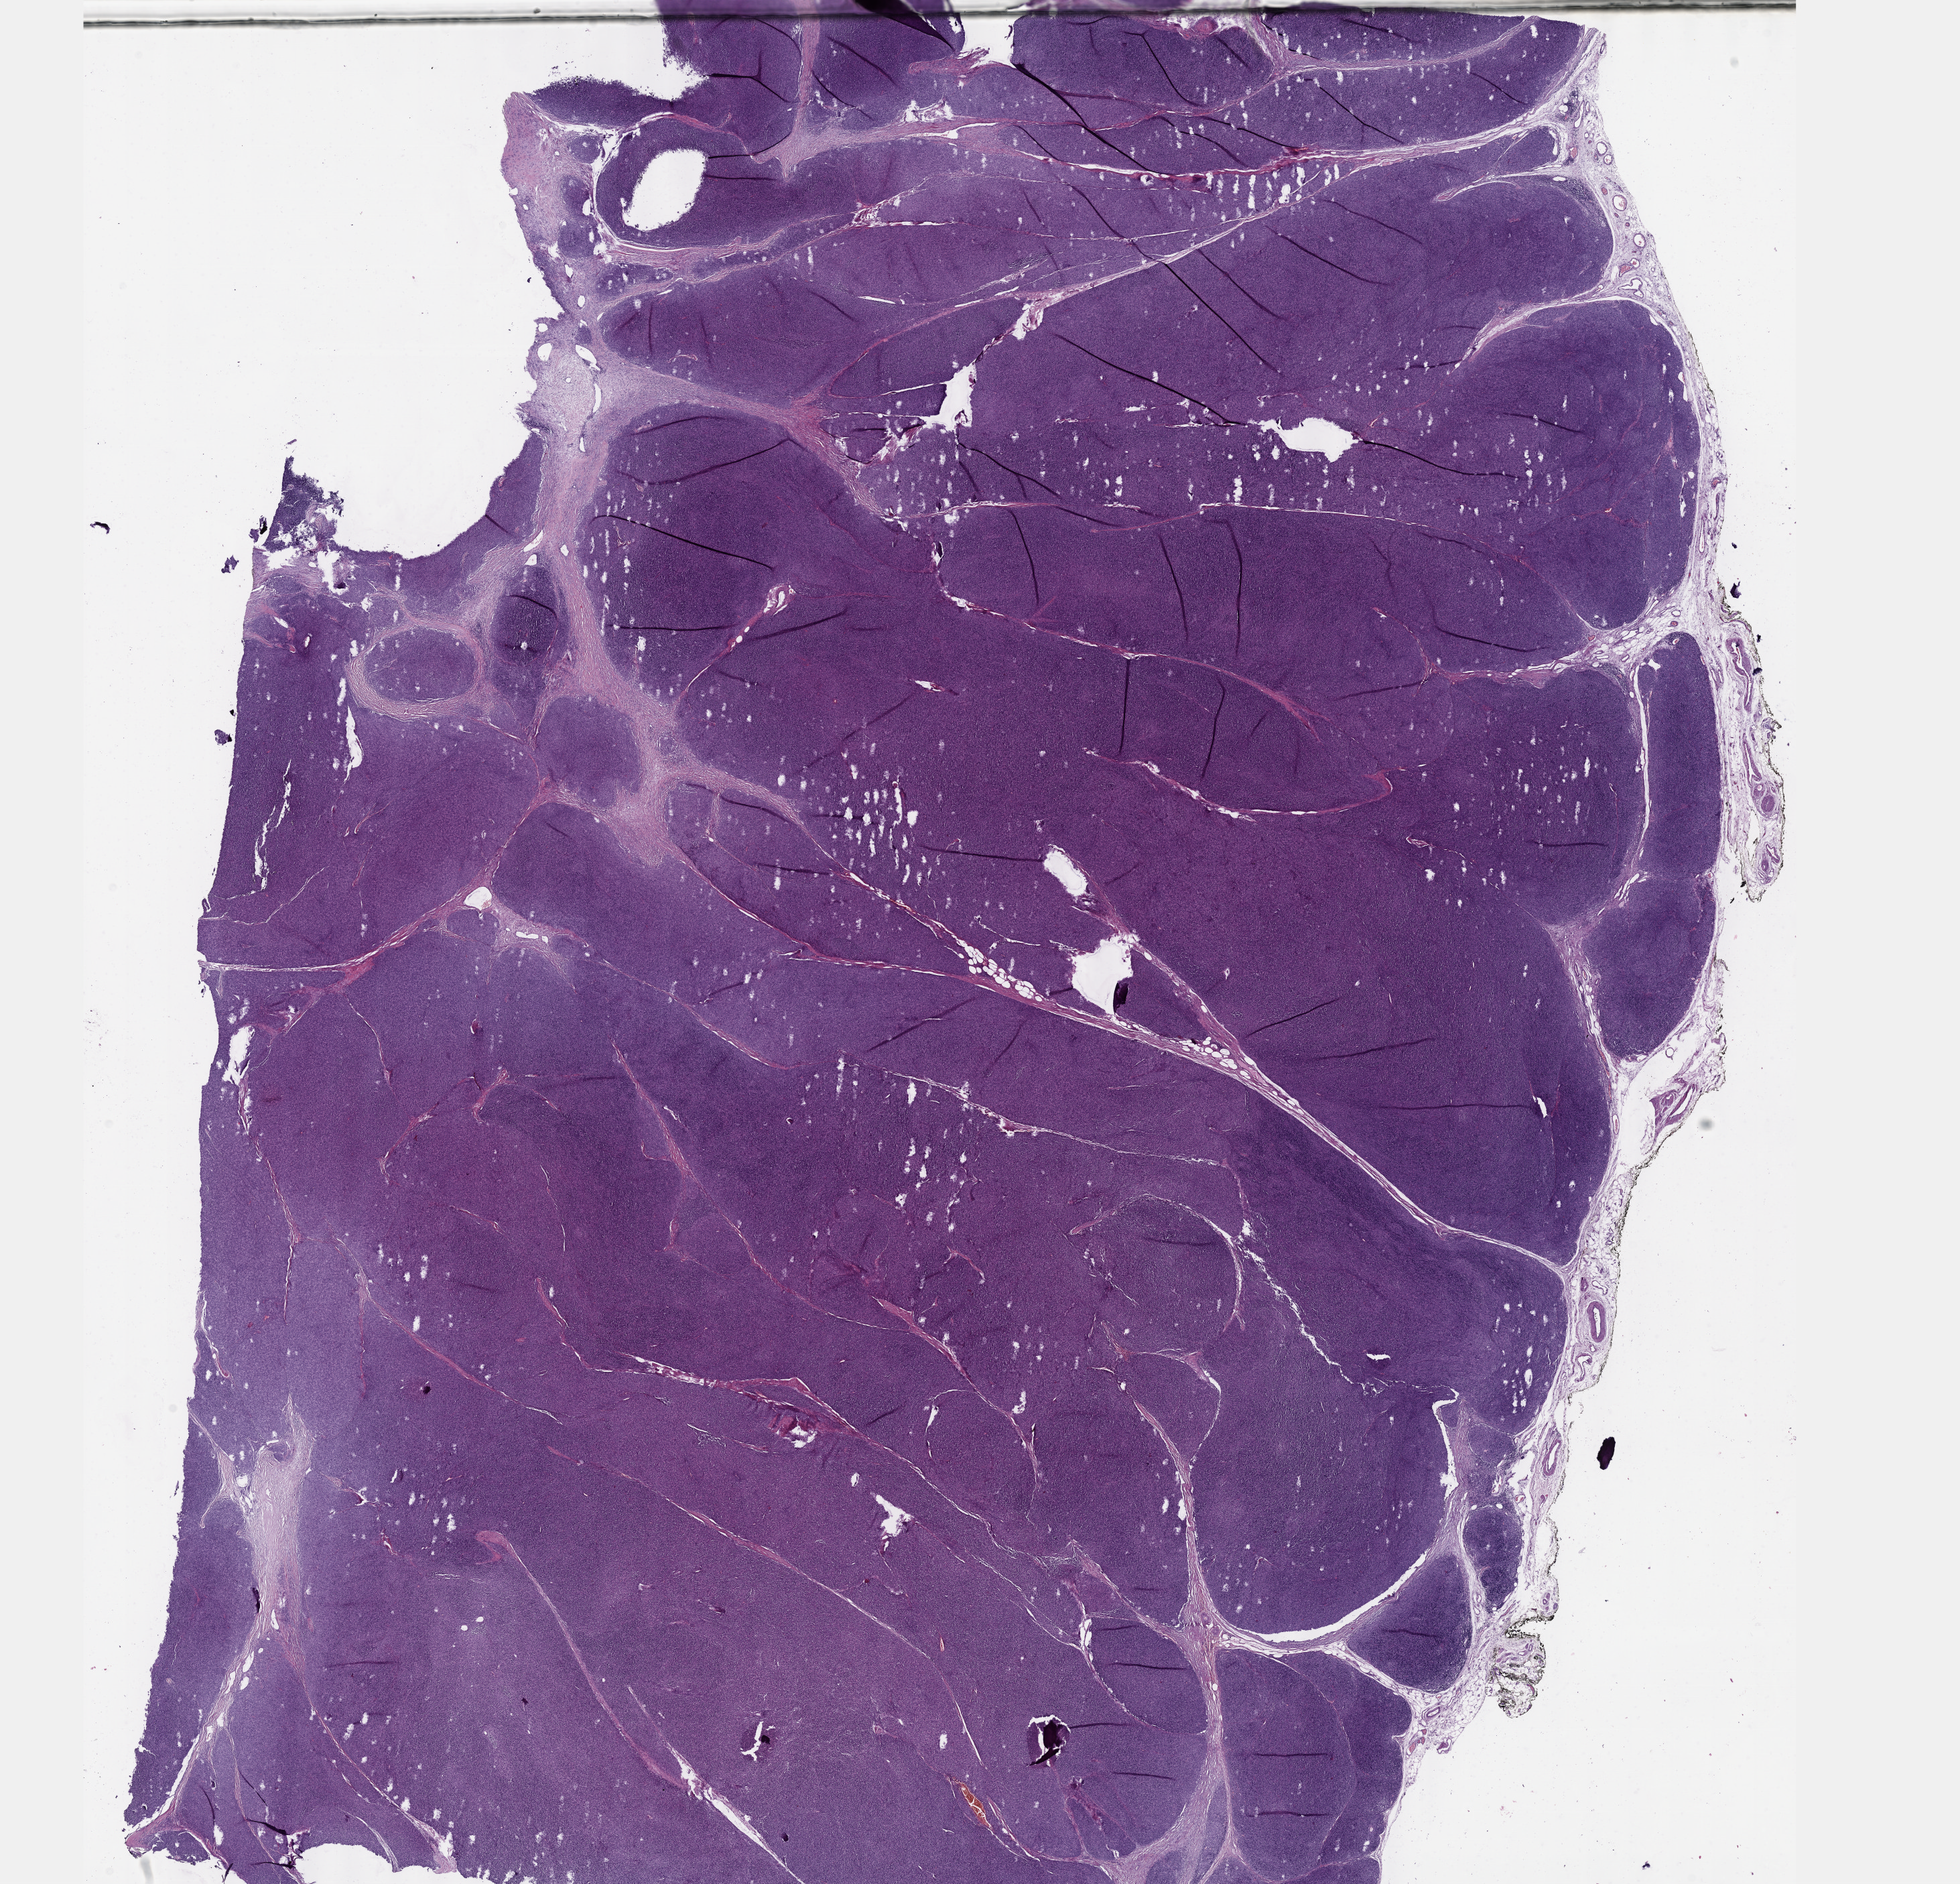
Whole-slide histology image, Hematoxylin and eosin (H&E) stained, a low-resolution overview of the entire scanned area, about 23.6 x 22.7 mm (from a 40x scan); formalin-fixed paraffin-embedded (FFPE) diagnostic section; thymus, primary tumour sample. Female patient; age at initial diagnosis 58 years.
Histologic diagnosis: Thymoma, type AB, malignant (anterior mediastinum).